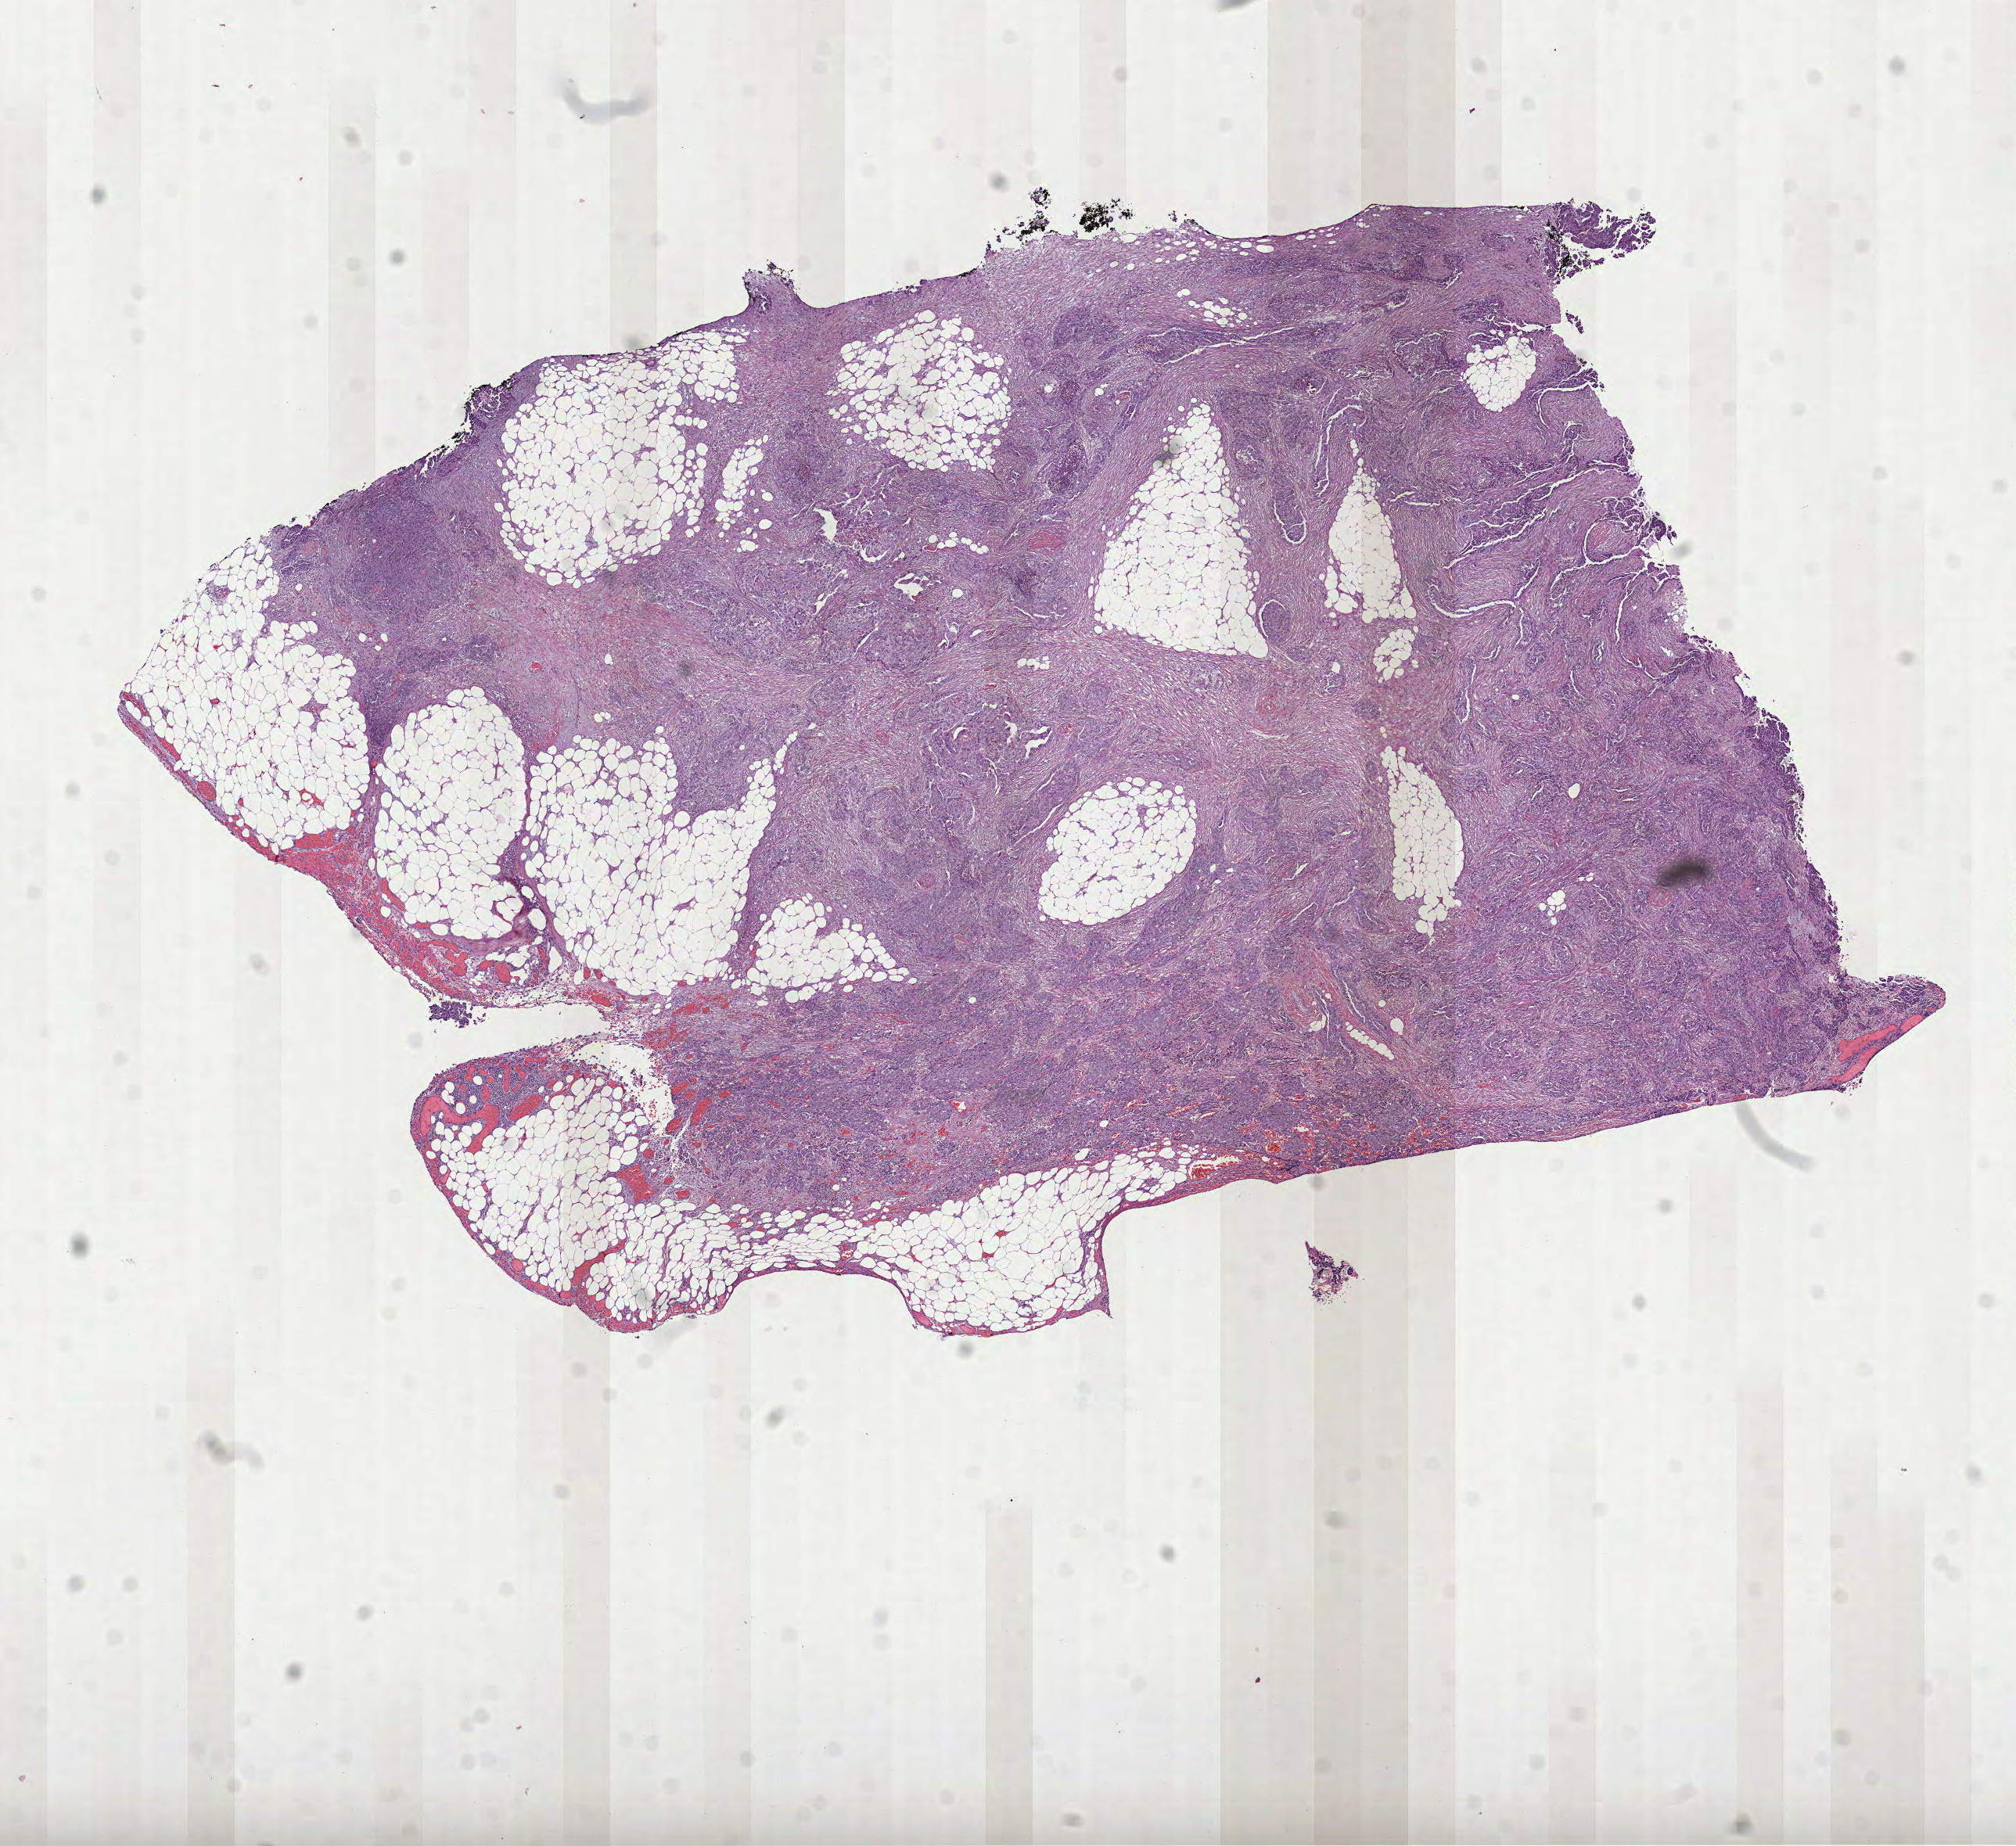
Whole-slide histology image, Hematoxylin and eosin (H&E) stained — a low-resolution overview of the entire scanned area, about 10.4 x 9.5 mm (from a 40x scan). Formalin-fixed paraffin-embedded (FFPE) diagnostic section. Primary tumour sample from the ovary. Patient: female, age at initial diagnosis 57 years. Histologic grade: G3 (poorly differentiated).
Laterality: bilateral. Diagnosis: Serous cystadenocarcinoma, NOS. FIGO stage: IIIC.